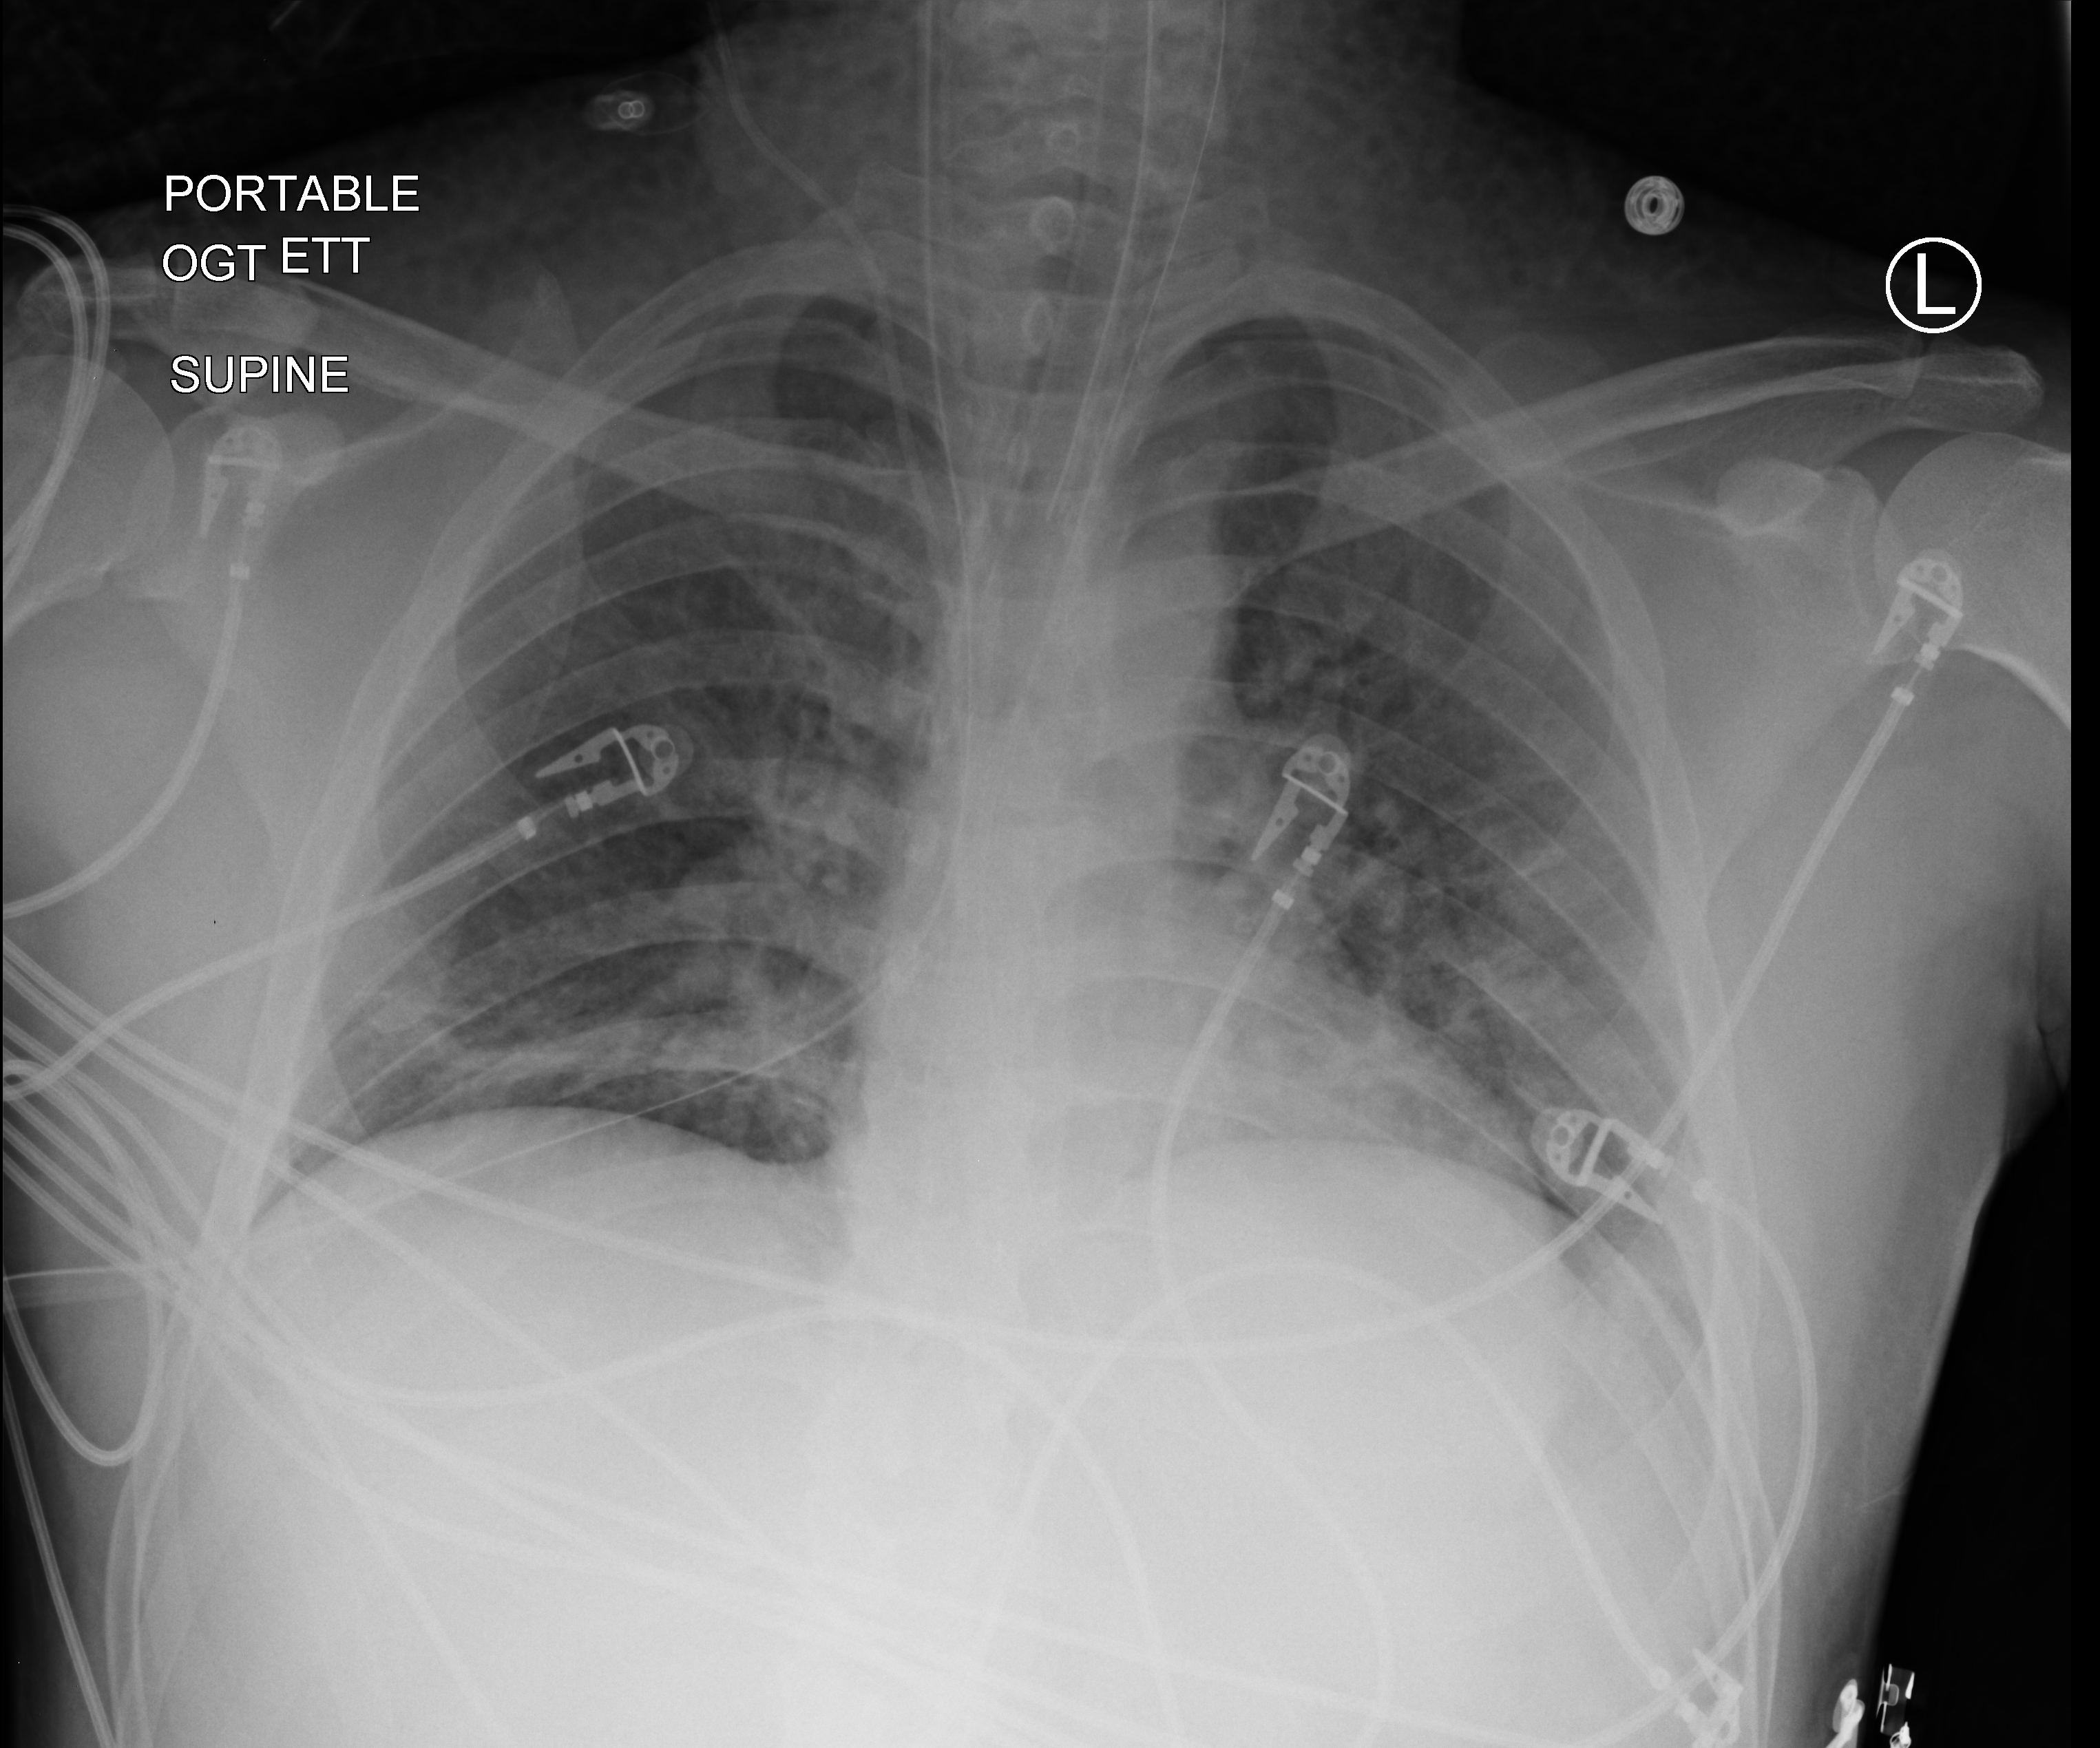
Bedside chest radiograph (computed radiography); anteroposterior (AP) projection. Male patient hospitalised with COVID-19, age 18–59 years.
From the hospital-stay record, not from the radiograph (when in the stay this image was taken is not recorded): mechanically ventilated during this hospital stay: yes; admitted to intensive care during this hospital stay: yes.